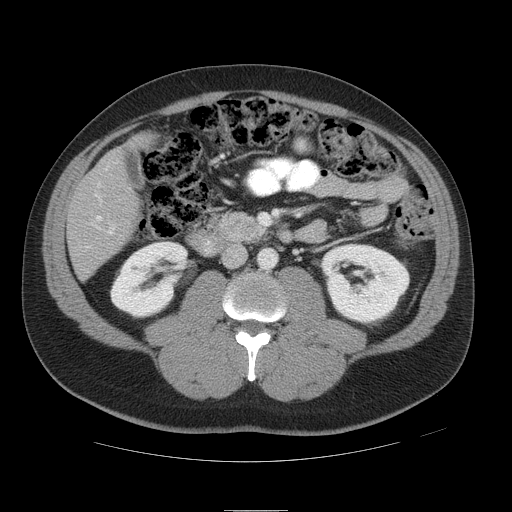
Contrast-enhanced abdominal CT, one axial slice. Slice 17 of 49 in the series (ordered by position). Intravenous contrast given. Soft-tissue window (W 400 / L 40 HU). 512 × 512 image matrix. Male patient, age 52 years. Case-level facts recorded for this patient, not image findings: diagnosis: colorectal cancer liver metastases, imaged before liver resection; multiple liver metastases: yes; largest metastasis: 5.1 cm; disease in both lobes: yes.
Outlined on this slice (expert manual segmentation):
- hepatic veins: box from (x=96, y=216) to (x=102, y=221) px
- liver: (x=69, y=153)–(x=138, y=277)
- portal vein (with intrahepatic branches): (x=94, y=165)–(x=114, y=235)